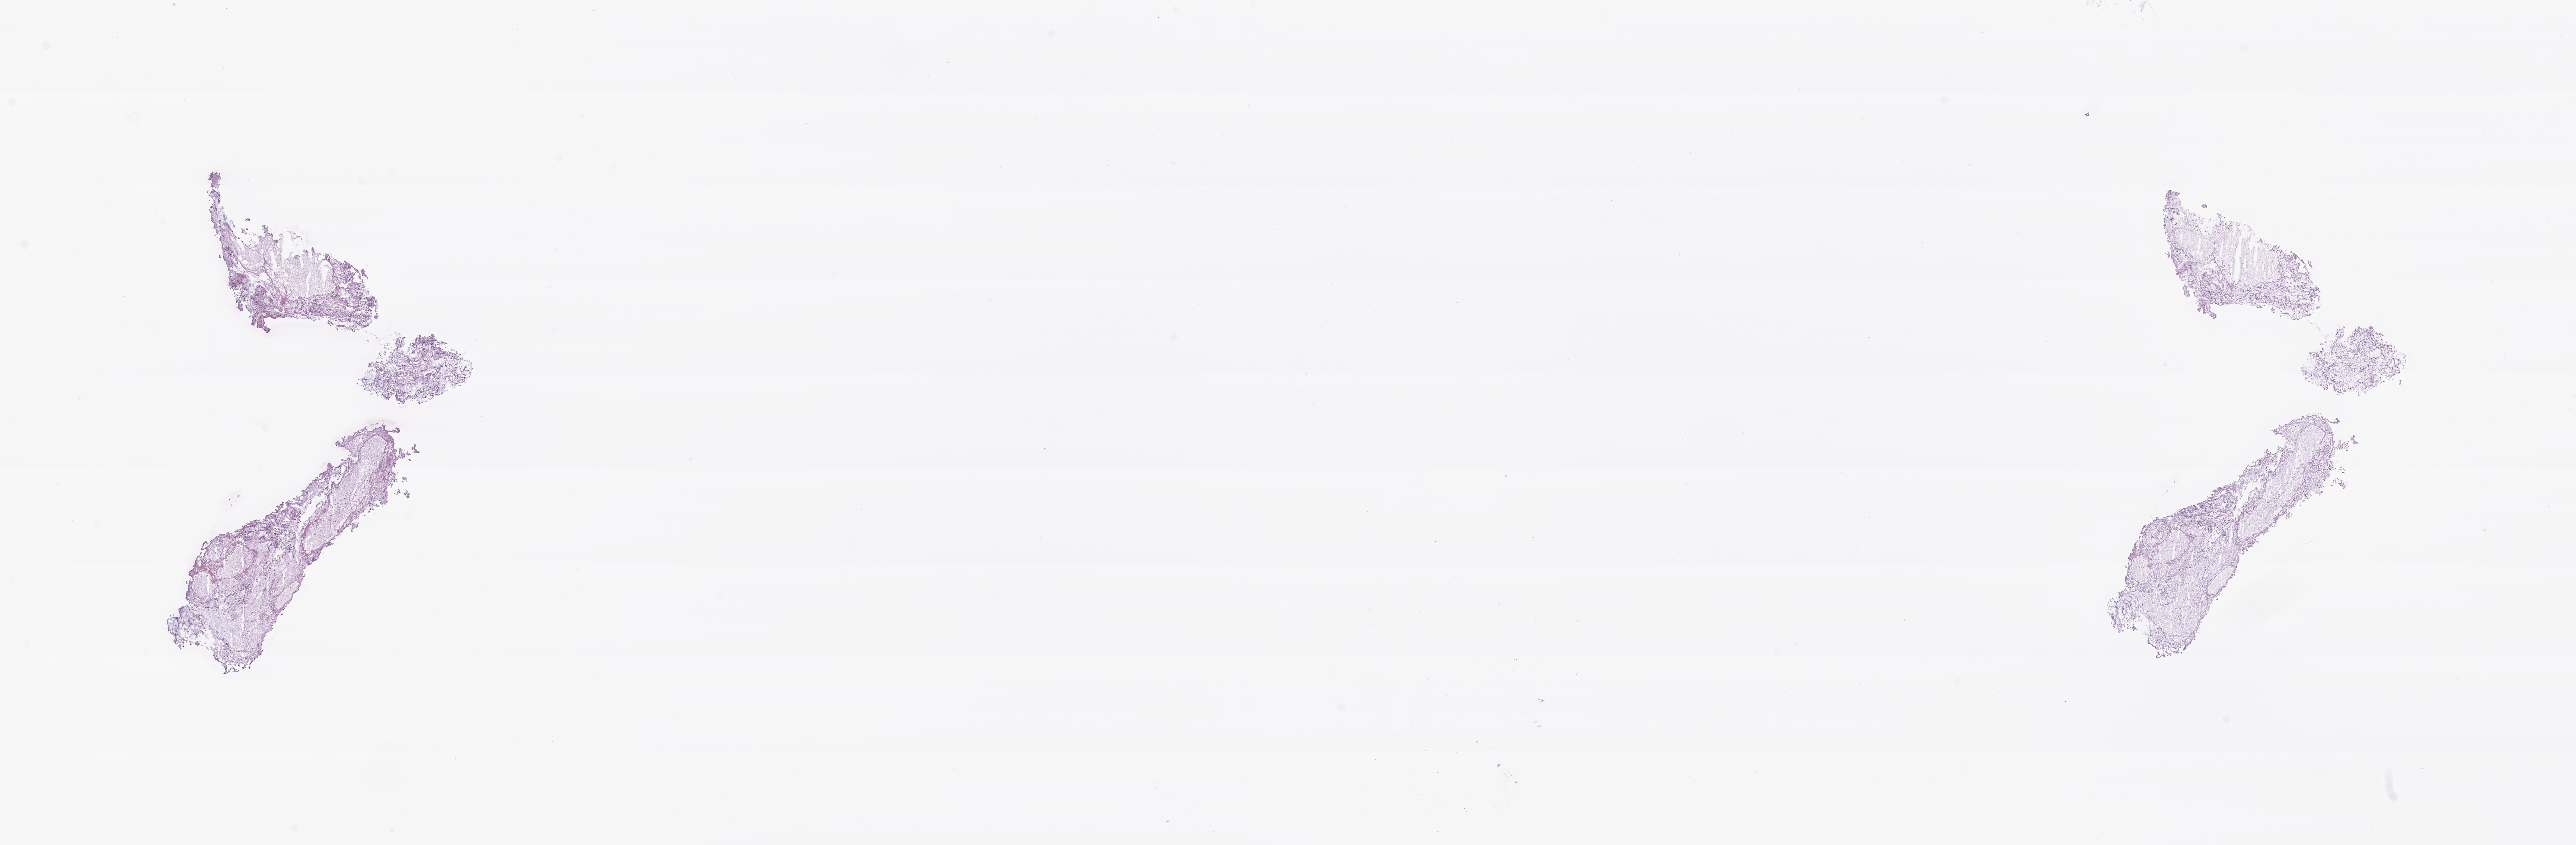
Digitized hematoxylin and eosin (H&E)-stained section of tumor tissue from the spinal cord, shown as a low-resolution overview of the whole scanned area (about 29.1 x 9.5 mm), frozen section (OCT-embedded). Male patient, age 112 months (9 years 4 months).
Diagnosis (ICD-O-3 morphology term): Myxopapillary ependymoma.